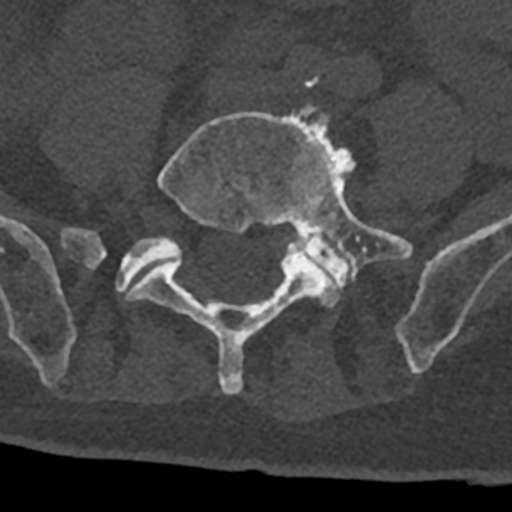
CT including the spine, one axial slice. Position 195 of 797 along the scan axis. Reconstruction kernel Br40s/3. Bone window (W 1800 / L 400 HU). 0.5 mm slice thickness. 512 × 512 image matrix, field of view 160 × 160 mm. Patient: male, 74 years. Case-level facts recorded for this patient, not image findings: primary cancer: renal.
Outlined on this slice (semi-automatic segmentation, software-assisted and operator-edited):
- L5 vertebra: box from (x=126, y=103) to (x=413, y=394) px